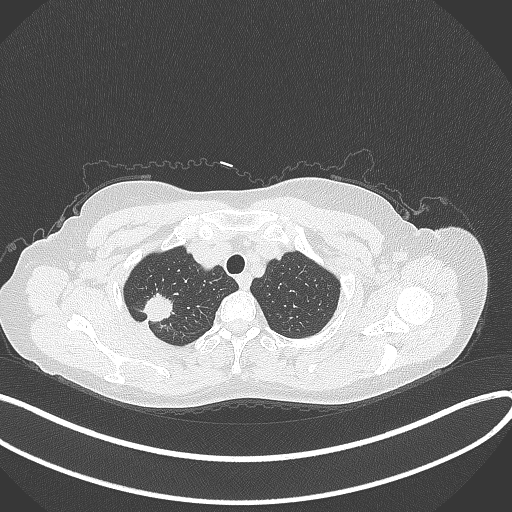
Chest CT, one axial slice; slice 316 of 337 in the series (ordered by position); reconstruction kernel B70f; lung window (W 1500 / L -600 HU); 1 mm slice thickness; 512 × 512 image matrix, field of view 400 × 400 mm. Female patient, age 50 years. Case-level facts recorded for this patient, not image findings: clinical TNM (as recorded): T1c N0 M0; histopathological grade: G2-3.
Outlined on this slice (rectangle marked by the reading radiologist):
- lung tumour (recorded histology: adenocarcinoma): bounding box [x1, y1, x2, y2] px = [137, 290, 177, 324]